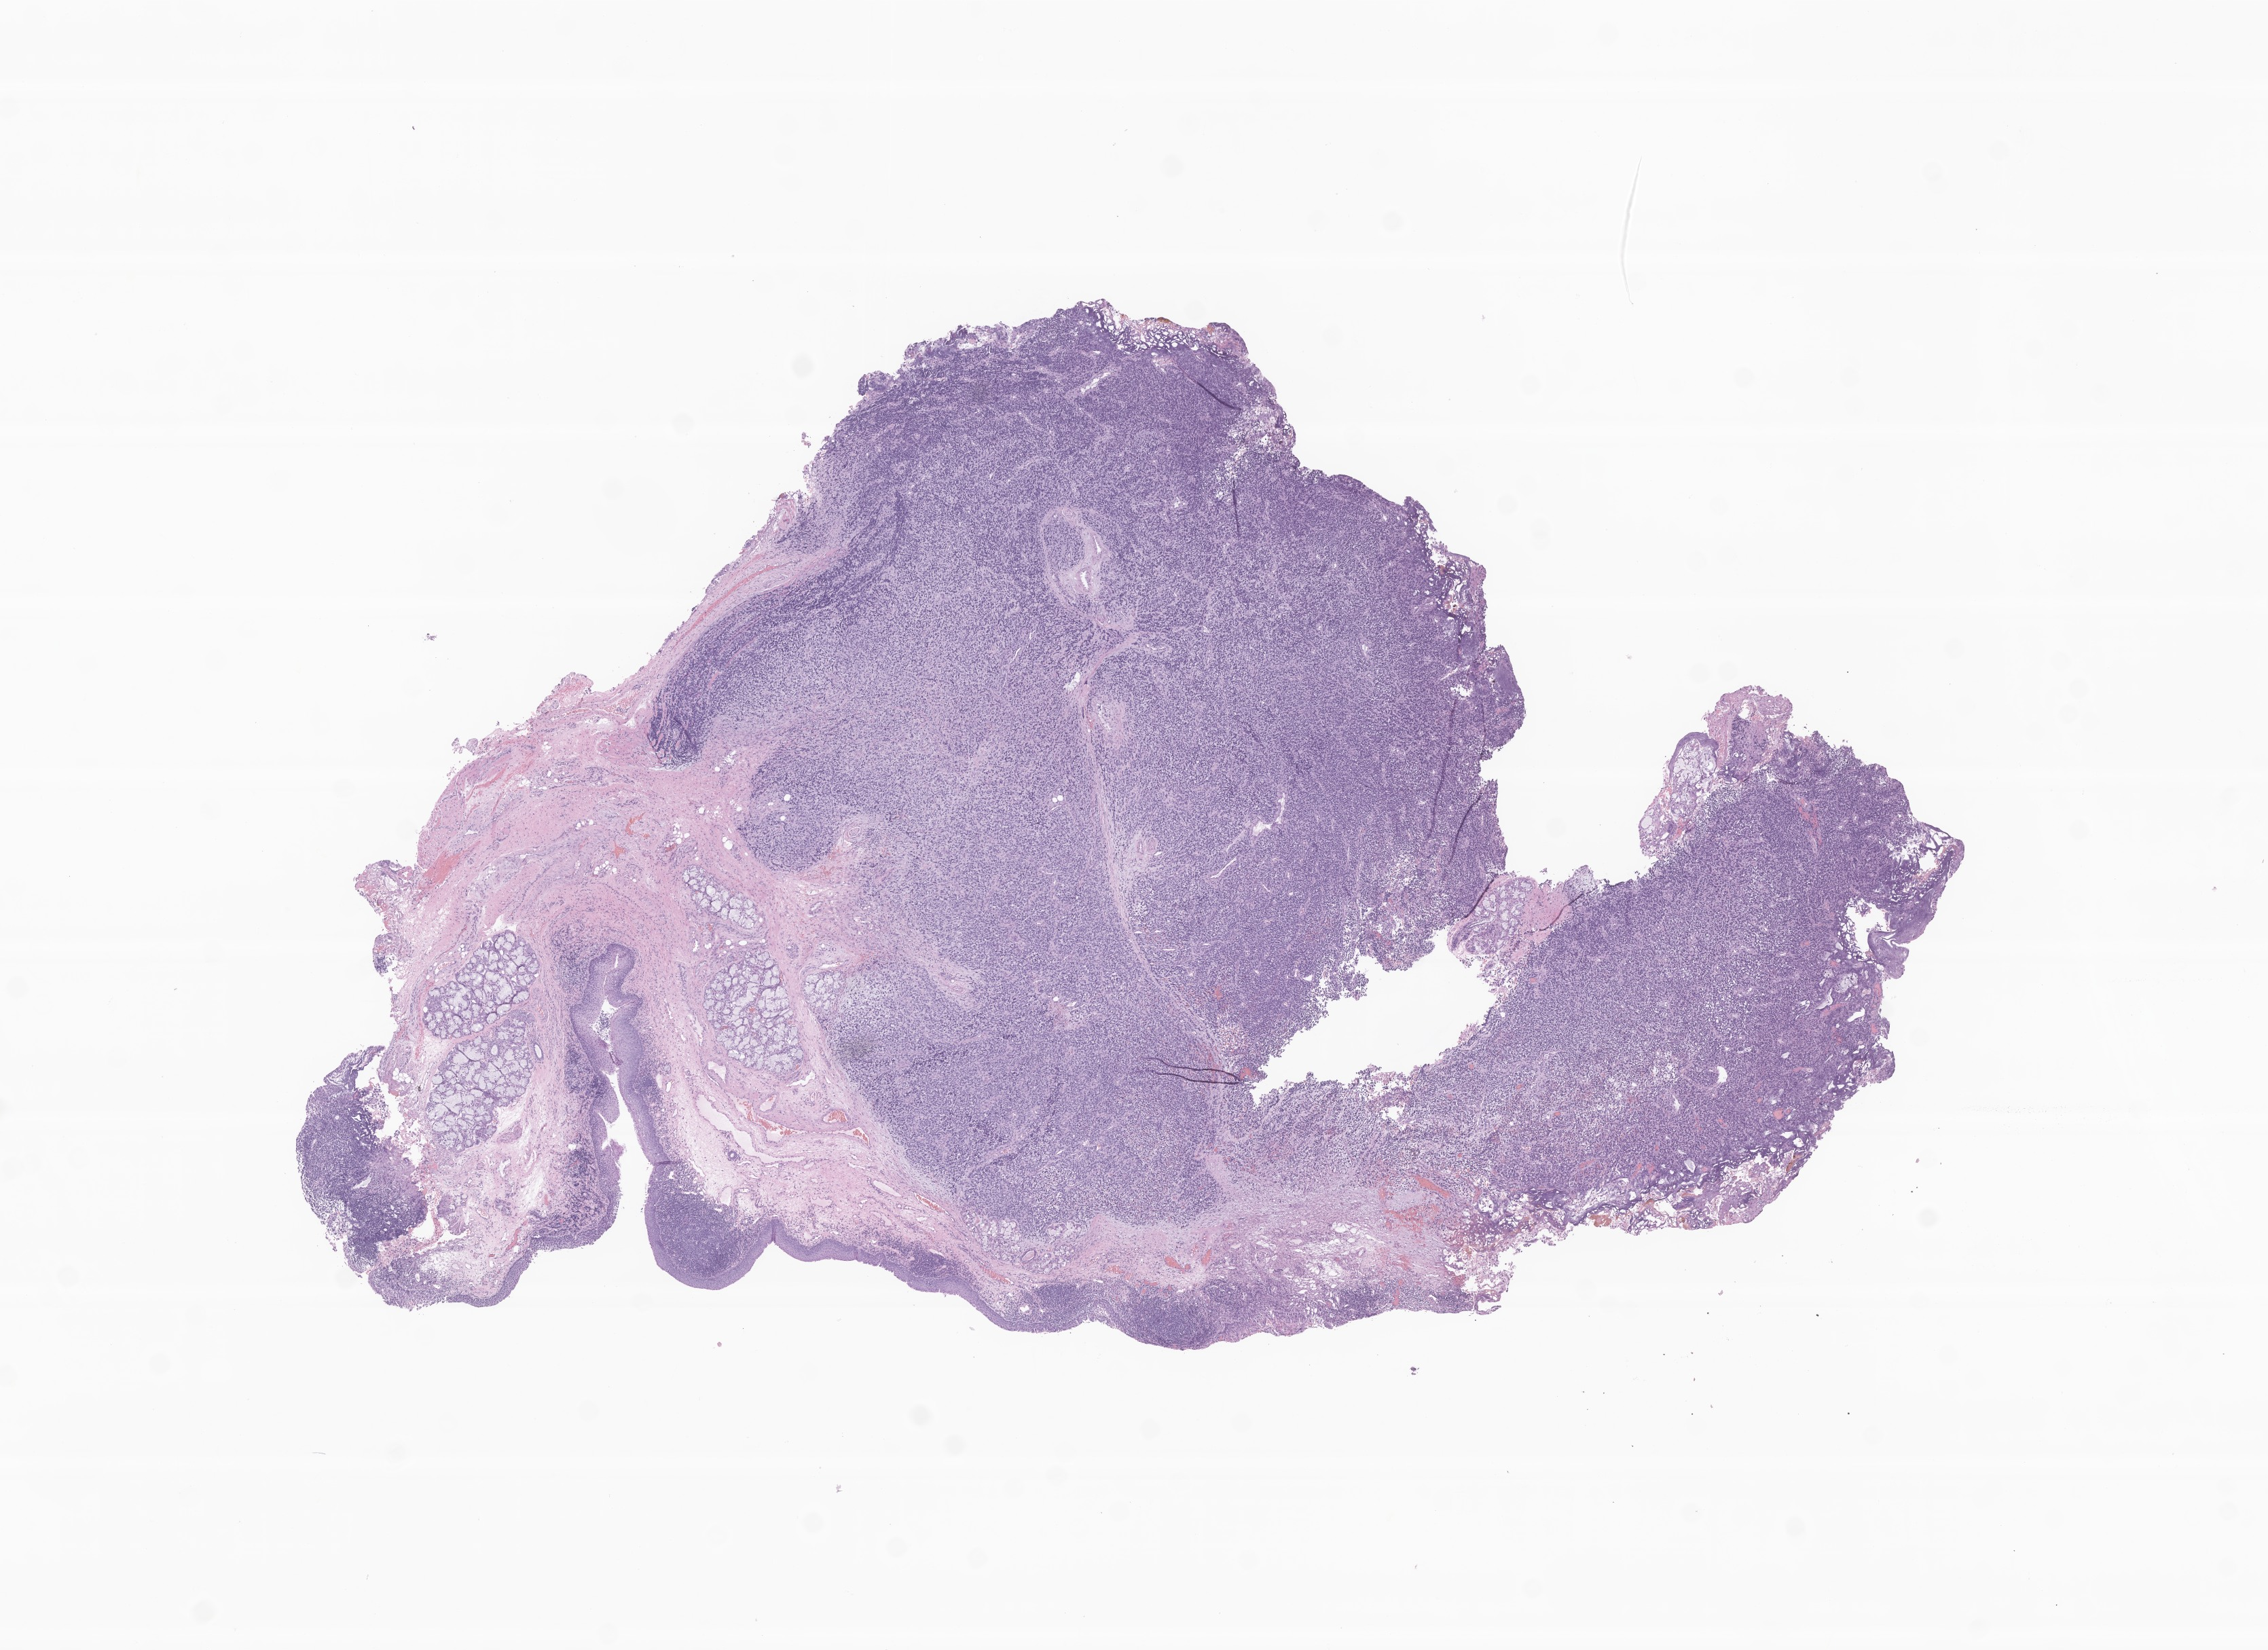
Whole-slide image, hematoxylin and eosin (H&E) stain of tumor tissue from the superior wall of nasopharynx, whole scanned area (about 14.1 x 10.2 mm) shown as a low-resolution overview, formalin-fixed, paraffin-embedded (FFPE) tissue. Female patient, age 962 days (about 2.6 years).
Diagnosis (ICD-O-3 morphology term): Rhabdomyosarcoma, NOS.